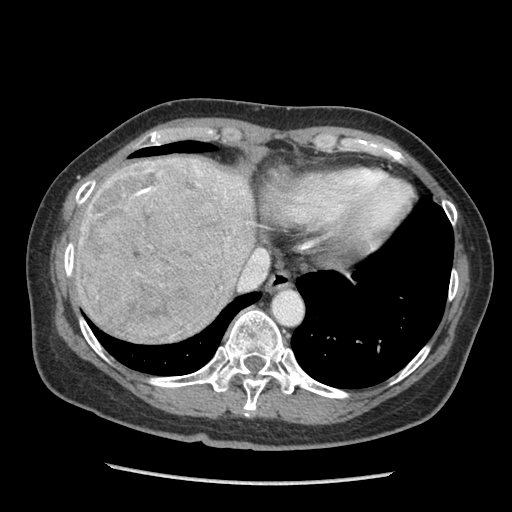
Contrast-enhanced abdominal CT (liver protocol), one axial slice. Slice 78 of 105 in the series (ordered by position). Reconstruction kernel STANDARD. Soft-tissue window (W 400 / L 40 HU). 2.5 mm slice thickness. 512 × 512 image matrix. Case-level facts recorded for this patient, not image findings: diagnosis: hepatocellular carcinoma (patient treated with transarterial chemoembolisation; whether this scan precedes or follows treatment is not stated here); TNM stage (as recorded): Stage-I; Child-Pugh class: A; tumour nodularity: uninodular.
Annotated regions visible in this slice (semi-automatic segmentation, software-assisted and operator-edited):
- liver parenchyma outside the tumour (the mass and vessels are separate outlines, so this box may not span the whole liver): box from (x=74, y=156) to (x=256, y=330) px
- mass: (x=77, y=158)–(x=231, y=343)
- liver vessels: (x=218, y=176)–(x=244, y=194)